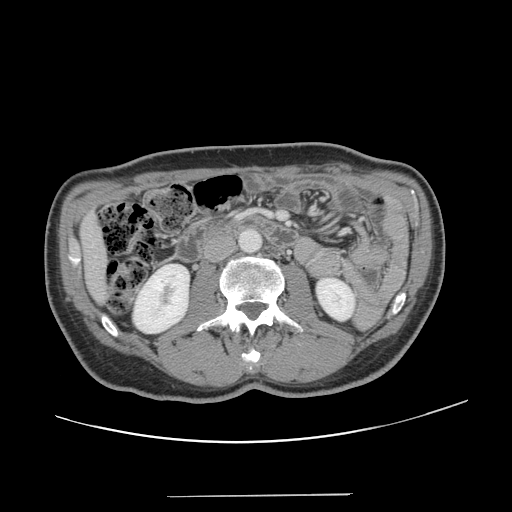
Contrast-enhanced abdominal CT, one axial slice; slice 45 of 131 in the series (ordered by position); intravenous contrast given; soft-tissue window (W 400 / L 40 HU); 512 × 512 image matrix. Male patient, age 60 years. Case-level facts recorded for this patient, not image findings: diagnosis: colorectal cancer liver metastases, imaged before liver resection; multiple liver metastases: no; largest metastasis: 2.5 cm; disease in both lobes: no.
Structures marked on this image (outlined manually by an expert reader):
- liver: box from (x=82, y=217) to (x=105, y=300) px
- planned liver remnant (the part of the liver to remain after resection): (x=82, y=217)–(x=105, y=299)